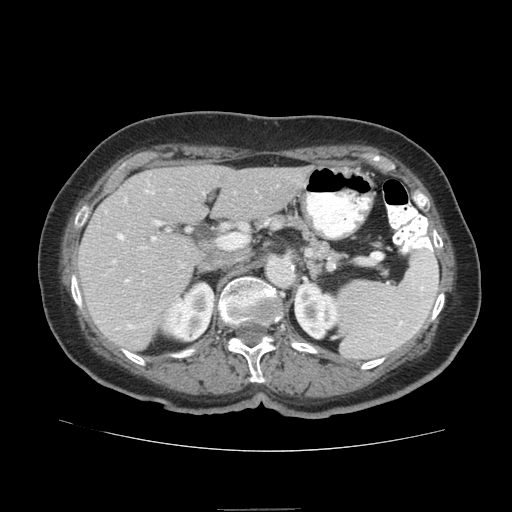
Contrast-enhanced abdominal CT (liver protocol), one axial slice. Slice 44 of 95 in the series (ordered by position). Reconstruction kernel STANDARD. 140 kVp. Soft-tissue window (W 400 / L 40 HU). 2.5 mm slice thickness. 512 × 512 image matrix. From the clinical record (not read from this slice): diagnosis: hepatocellular carcinoma (patient treated with transarterial chemoembolisation; whether this scan precedes or follows treatment is not stated here); TNM stage (as recorded): Stage-IVA; Child-Pugh class: B; tumour differentiation: moderately differentiated.
Annotated regions visible in this slice (semi-automatically segmented with operator editing):
- liver parenchyma outside the tumour (the mass and vessels are separate outlines, so this box may not span the whole liver): bounding box <76,164,312,350> (left, top, right, bottom; pixels)
- liver vessels: <113,190,162,329>